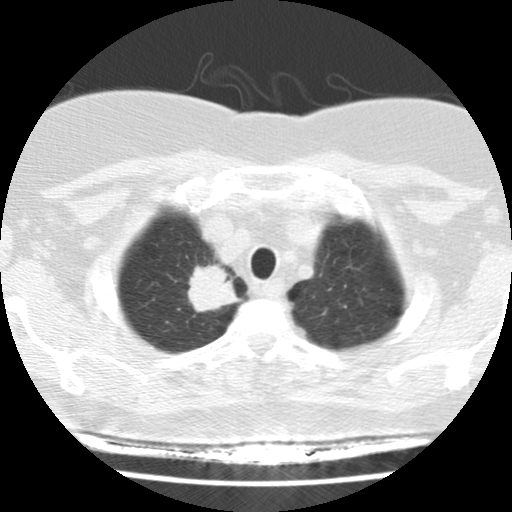
Low-dose screening chest CT, one axial slice; slice 131 of 148 in the series (ordered by position); lung window (W 1500 / L -600 HU); 2.5 mm slice thickness; 512 × 512 image matrix, field of view 281 × 281 mm.
Outlined on this slice (outlined manually by an expert reader):
- lesion 1 (tumor, upper lobe of right lung): bounding box [x1, y1, x2, y2] px = [188, 264, 241, 312]